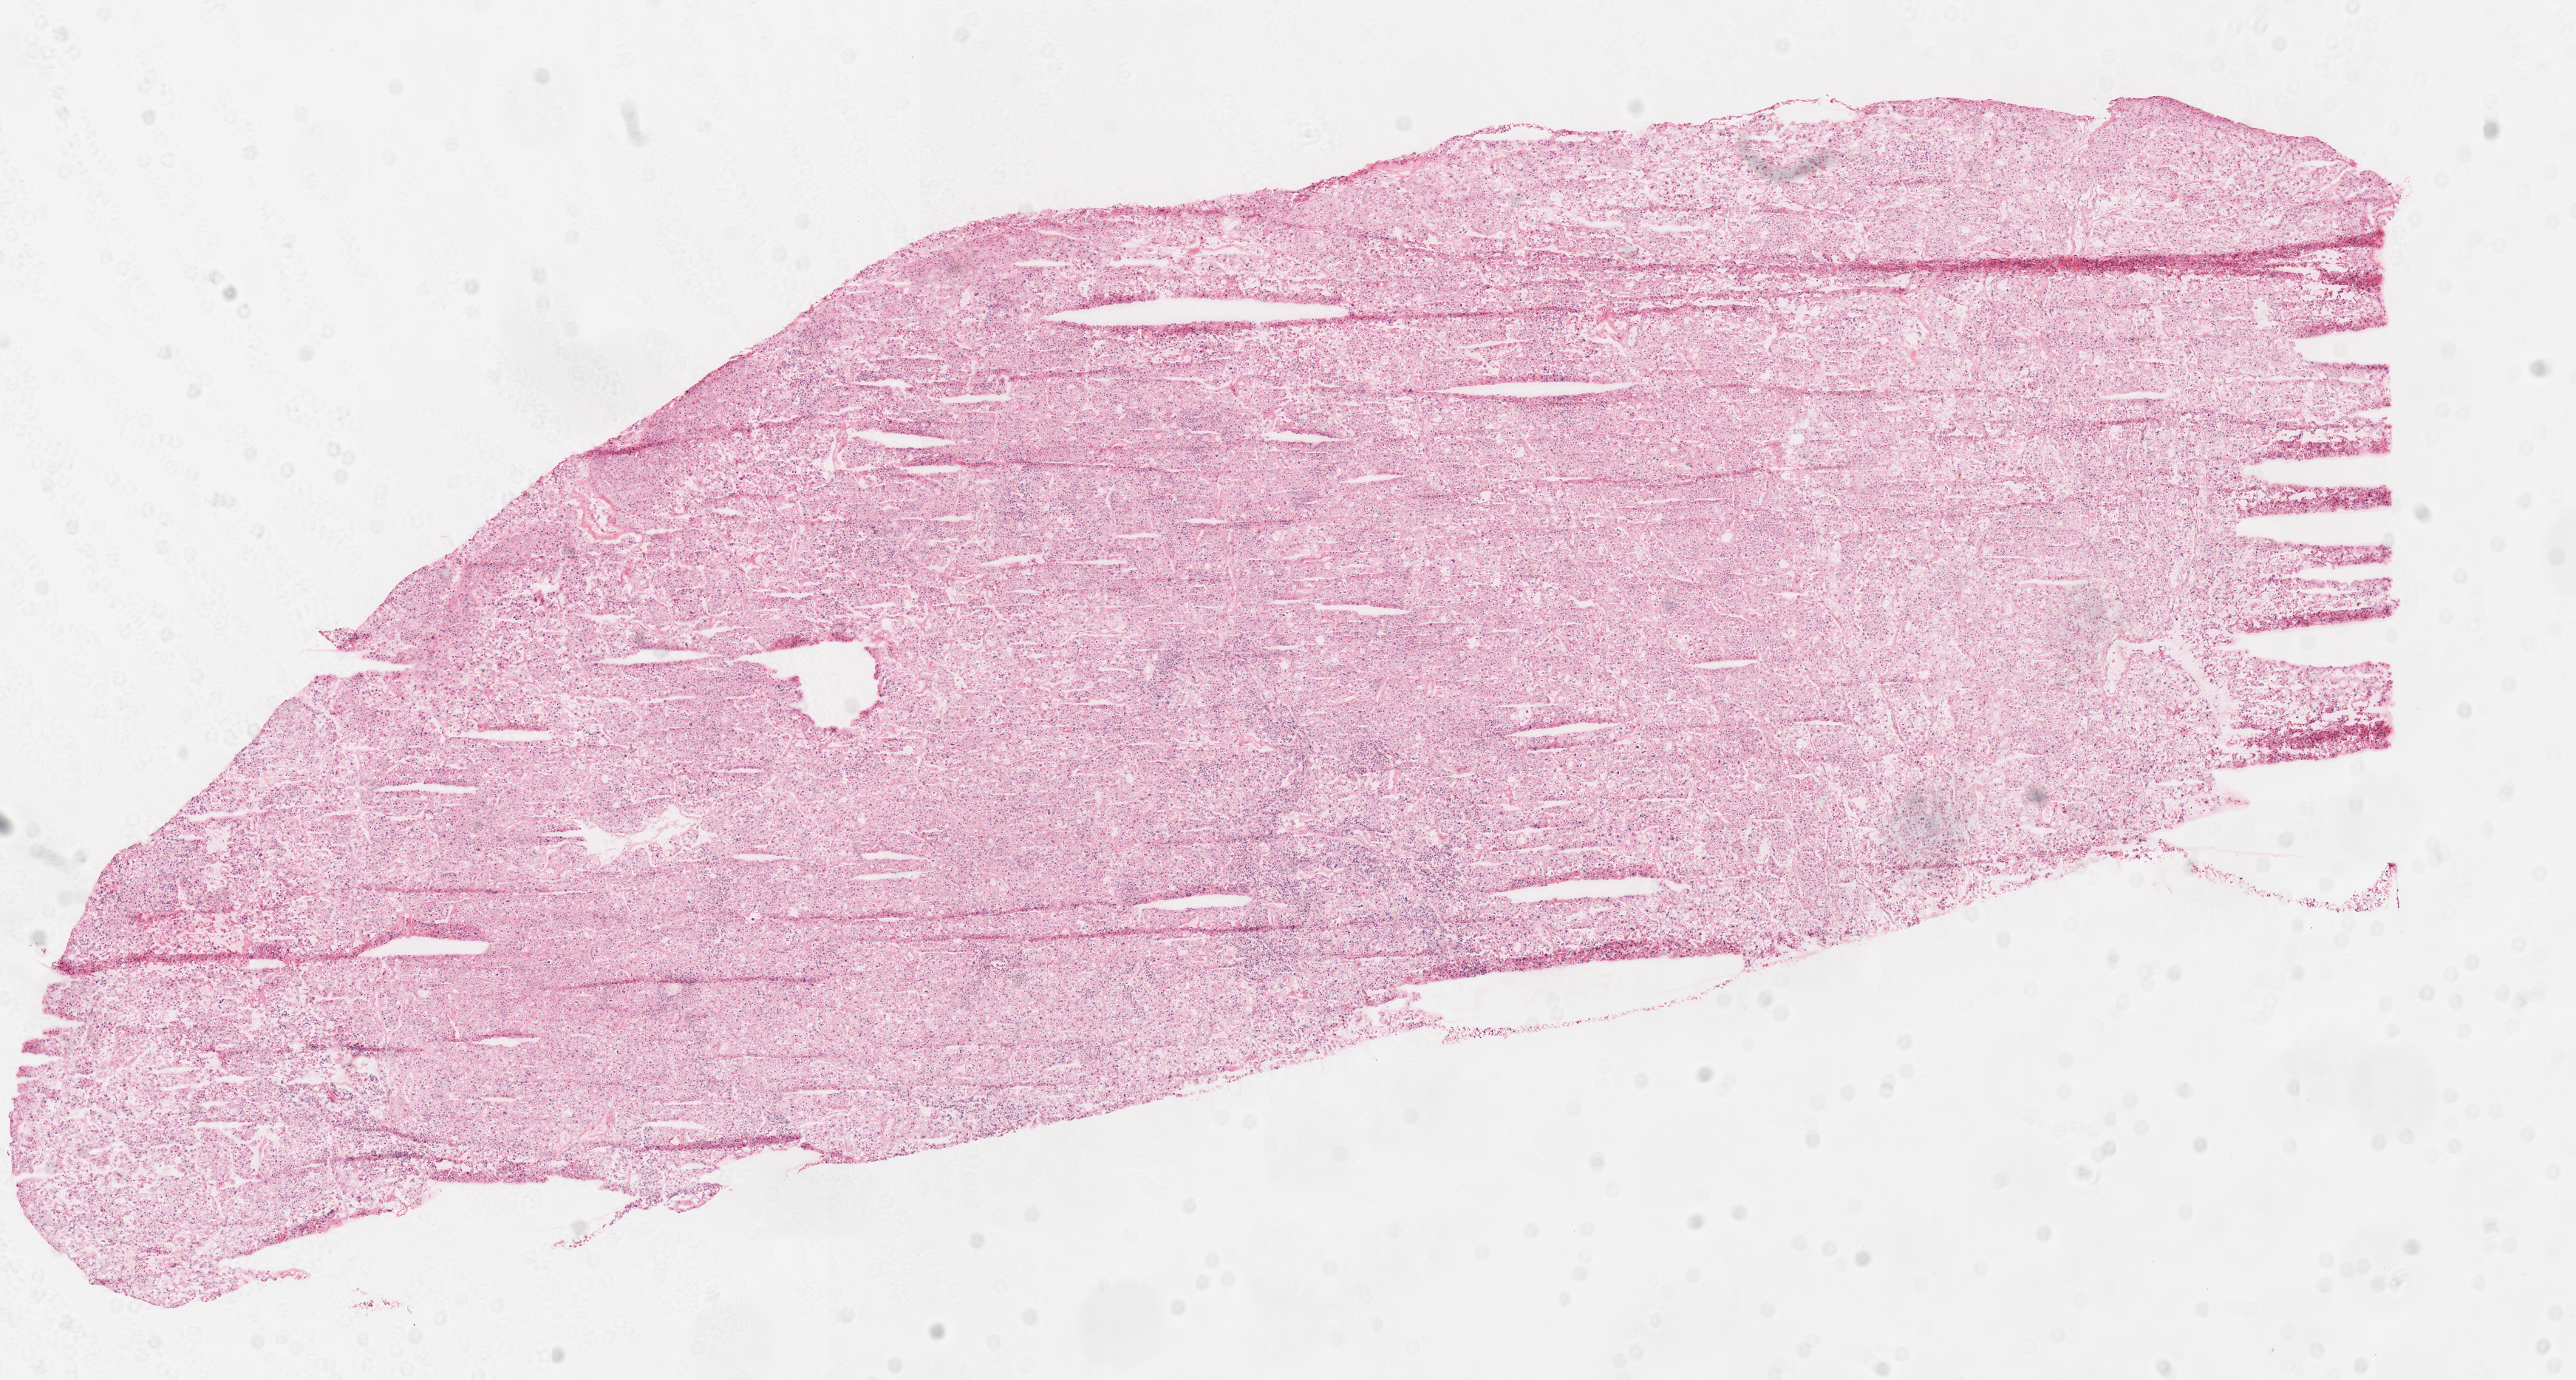
Whole-slide histology image, H&E-stained — whole scanned area (about 13.7 x 7.3 mm, from a 40x scan) shown as a low-resolution overview. Frozen section. Kidney, primary tumour sample. Female, age 41 years at initial diagnosis. Slide review estimates, as recorded: tumour cells 100%, tumour nuclei 95%, normal cells 0%, stromal cells 0%, necrosis 0%. Infiltration values recorded for this section: lymphocyte infiltration 0%, monocyte infiltration 0%, neutrophil infiltration 0%.
AJCC pathologic stage: II (5th edition). Laterality: right. Diagnosis: Renal cell carcinoma, chromophobe type. TNM: T2 N0.